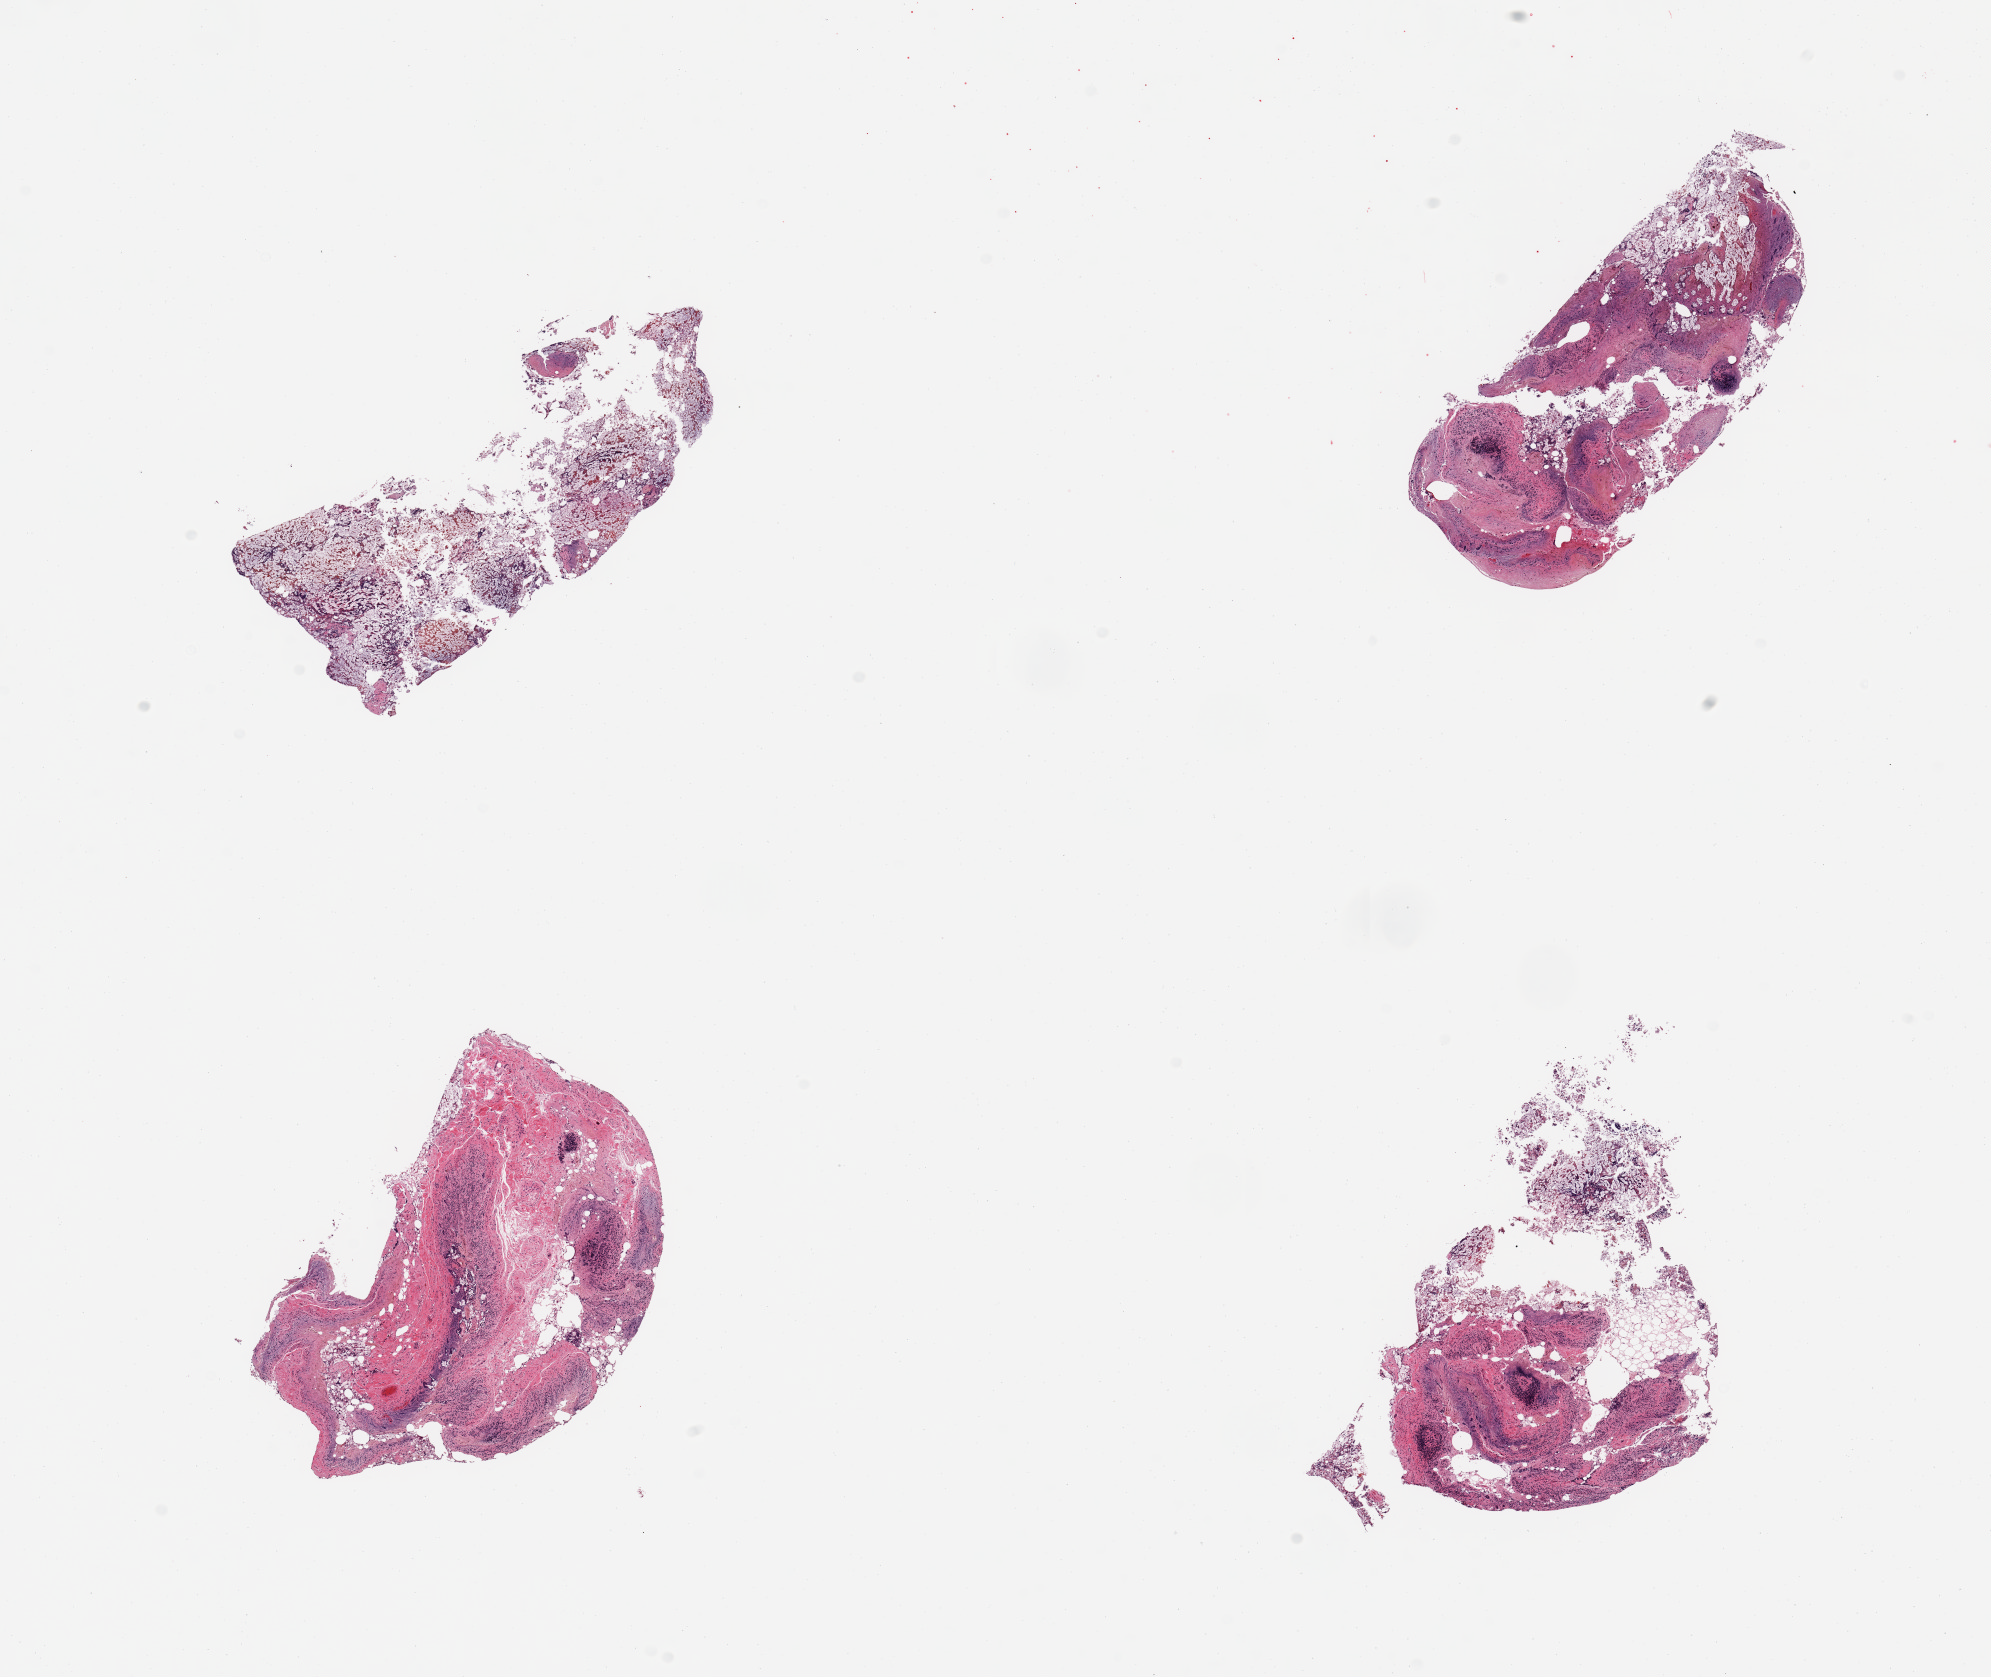
Digitized H&E-stained section, brightfield — whole scanned area (about 15.8 x 13.3 mm) shown as a low-resolution overview; PAXgene-fixed, paraffin-embedded tissue; section of ileum (target tissue); donor tissue sample. Donor: female.
Reviewer comment on this tissue sample: 4 pieces markedly autolyzed, correct targeet; insufficient target lymphoid elements.